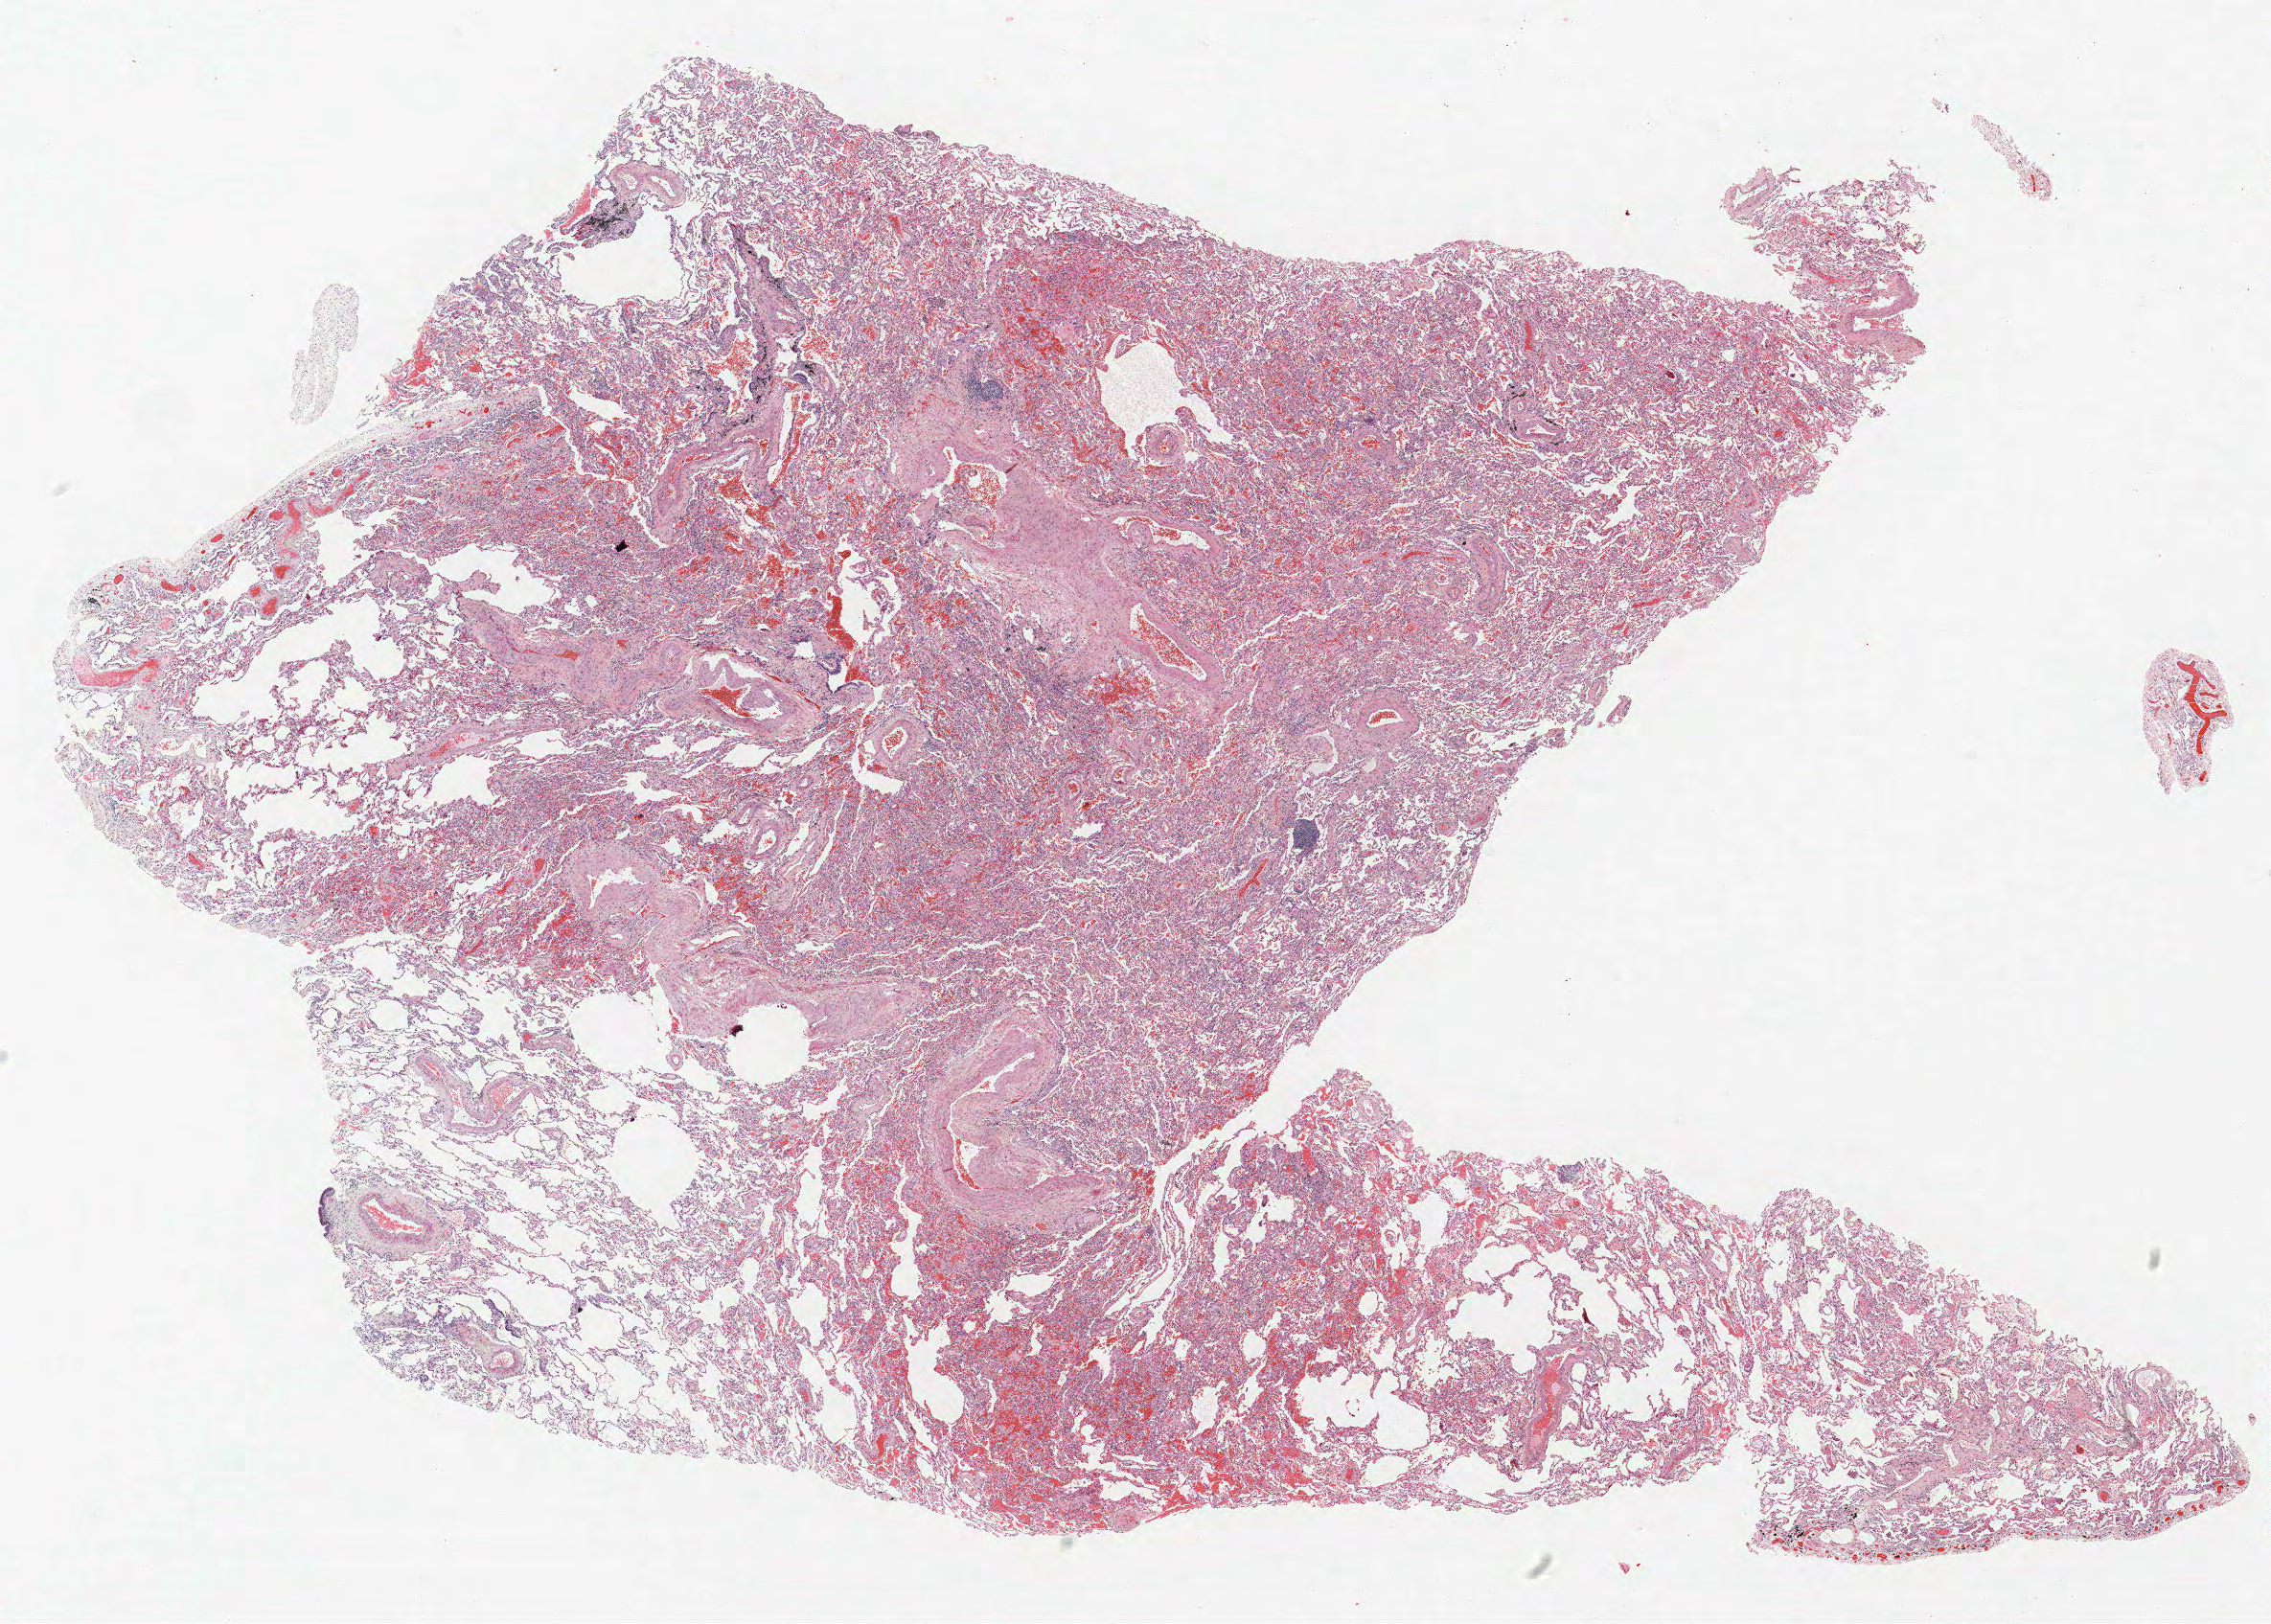
Hematoxylin and eosin (H&E) stained whole-slide image, whole scanned area (about 19.0 x 13.6 mm, acquisition: 40x scan) shown as a low-resolution overview, FFPE section, lung tissue. Male patient, aged 68 at enrolment. Former smoker at enrolment. Grade: poorly differentiated (G3).
Participant's lung-cancer diagnosis: Squamous cell carcinoma, NOS (ICD-O-3 8070/3). Primary tumour location (clinical record): left lower lobe. Tumour size (pathology): 40 mm. Stage (AJCC 6th edition): IIB.